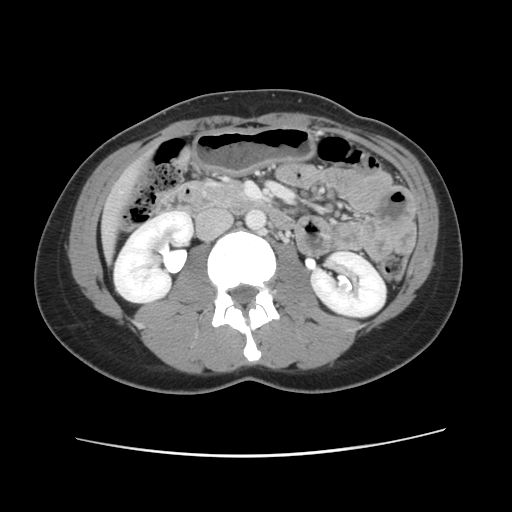
Contrast-enhanced abdominal CT, one axial slice; 120 kVp; intravenous contrast given; soft-tissue window (W 400 / L 40 HU); 2.5 mm slice thickness; 512 × 512 image matrix, field of view 339 × 339 mm. Female patient, age 33 years. From the clinical record (not read from this slice): diagnosis: colorectal cancer liver metastases, imaged before liver resection; multiple liver metastases: yes; largest metastasis: 4.5 cm.
Structures marked on this image (expert manual segmentation):
- liver: bounding box (x1, y1, x2, y2) in pixels: (101, 160, 146, 259)
- planned liver remnant (the part of the liver to remain after resection): (106, 249, 110, 258)